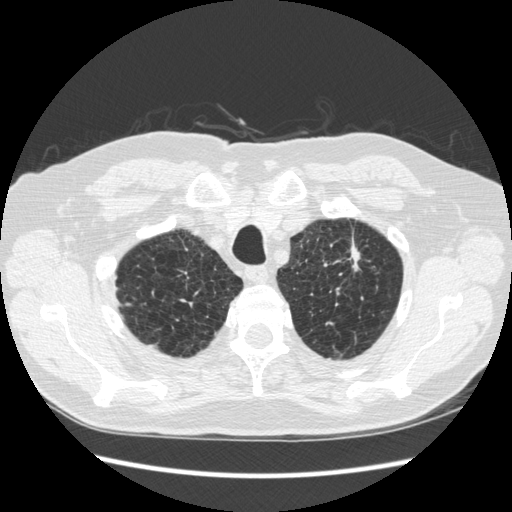
Chest CT (low-dose screening protocol), one axial image. Third annual screen. Lung window (W 1500 / L -600 HU). 1.25 mm slice thickness. Slice 36 of 267 in the series. Male, age 70 years at enrolment.
Expert-annotated lung lesion, box from (x=324, y=227) to (x=378, y=292) px. The screening reader recorded 2 non-calcified nodules or masses ≥4 mm on this exam; which of them this box marks is not recorded. Later outcome: lung cancer diagnosed 92 days after this screen — squamous cell carcinoma, NOS, left upper lobe, moderately differentiated (G2), stage IA (AJCC 6th edition), 18 mm at pathology.